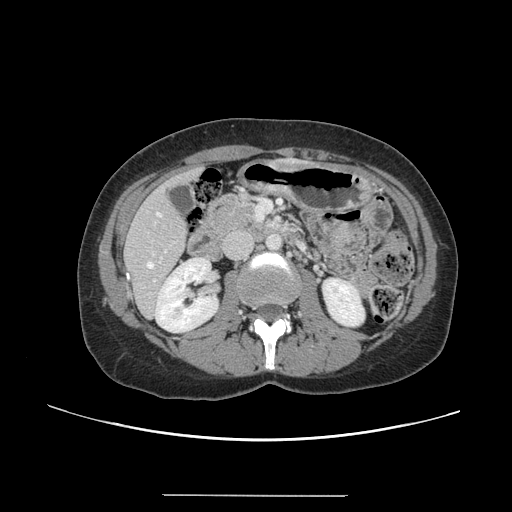
Contrast-enhanced abdominal CT, one axial slice; 120 kVp; intravenous contrast given; soft-tissue window (W 400 / L 40 HU); 512 × 512 image matrix, field of view 380 × 380 mm. Female patient, age 53 years. From the clinical record (not read from this slice): diagnosis: colorectal cancer liver metastases, imaged before liver resection; multiple liver metastases: yes; largest metastasis: 1.1 cm; disease in both lobes: no.
Structures marked on this image (outlined manually by an expert reader):
- hepatic veins: bounding box <147,212,161,268> (left, top, right, bottom; pixels)
- liver: <126,168,203,316>
- planned liver remnant (the part of the liver to remain after resection): <126,168,202,313>
- portal vein (with intrahepatic branches): <153,250,167,283>